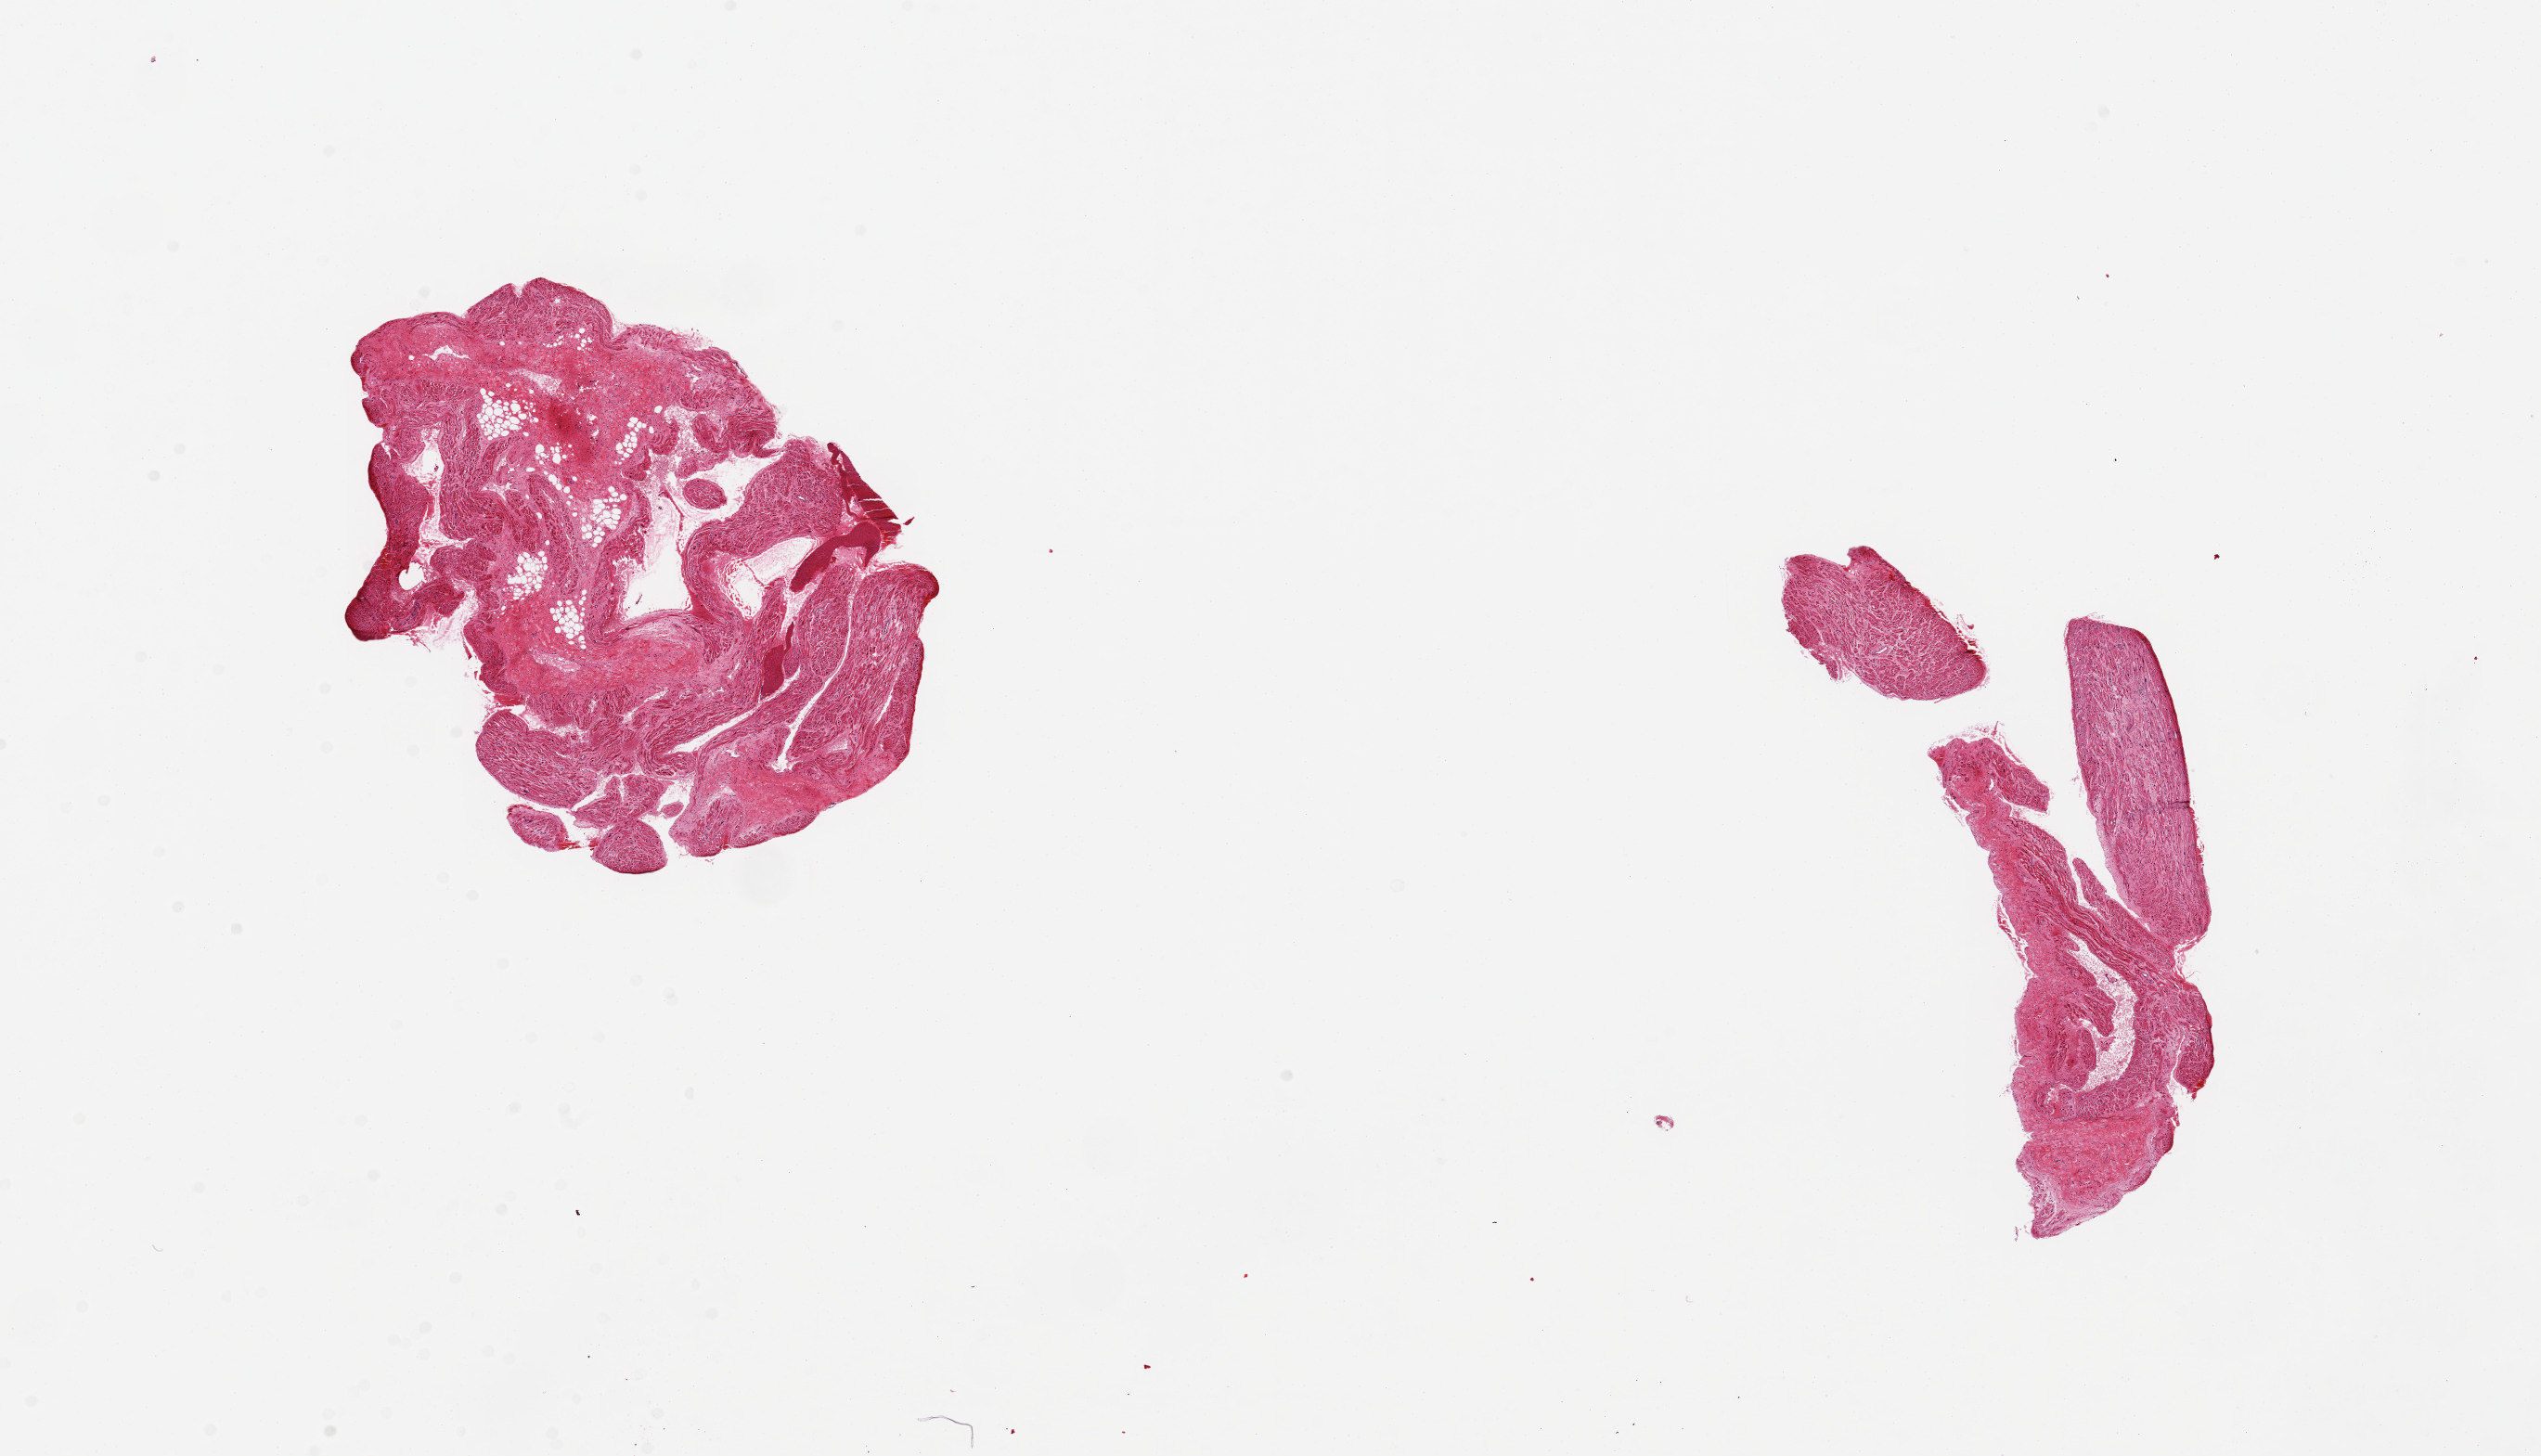
Whole-slide image, haematoxylin and eosin stain, low-resolution overview of the scanned area, about 21.7 x 12.4 mm. PAXgene-fixed paraffin-embedded (PFPE) section. Sampled site (target tissue): auricular appendage. Donor tissue sample. Donor: male.
Reviewer comment on this tissue sample: 2 pieces, 6x4 & 6x3mm; smaller has fibrous nodule ~25%.